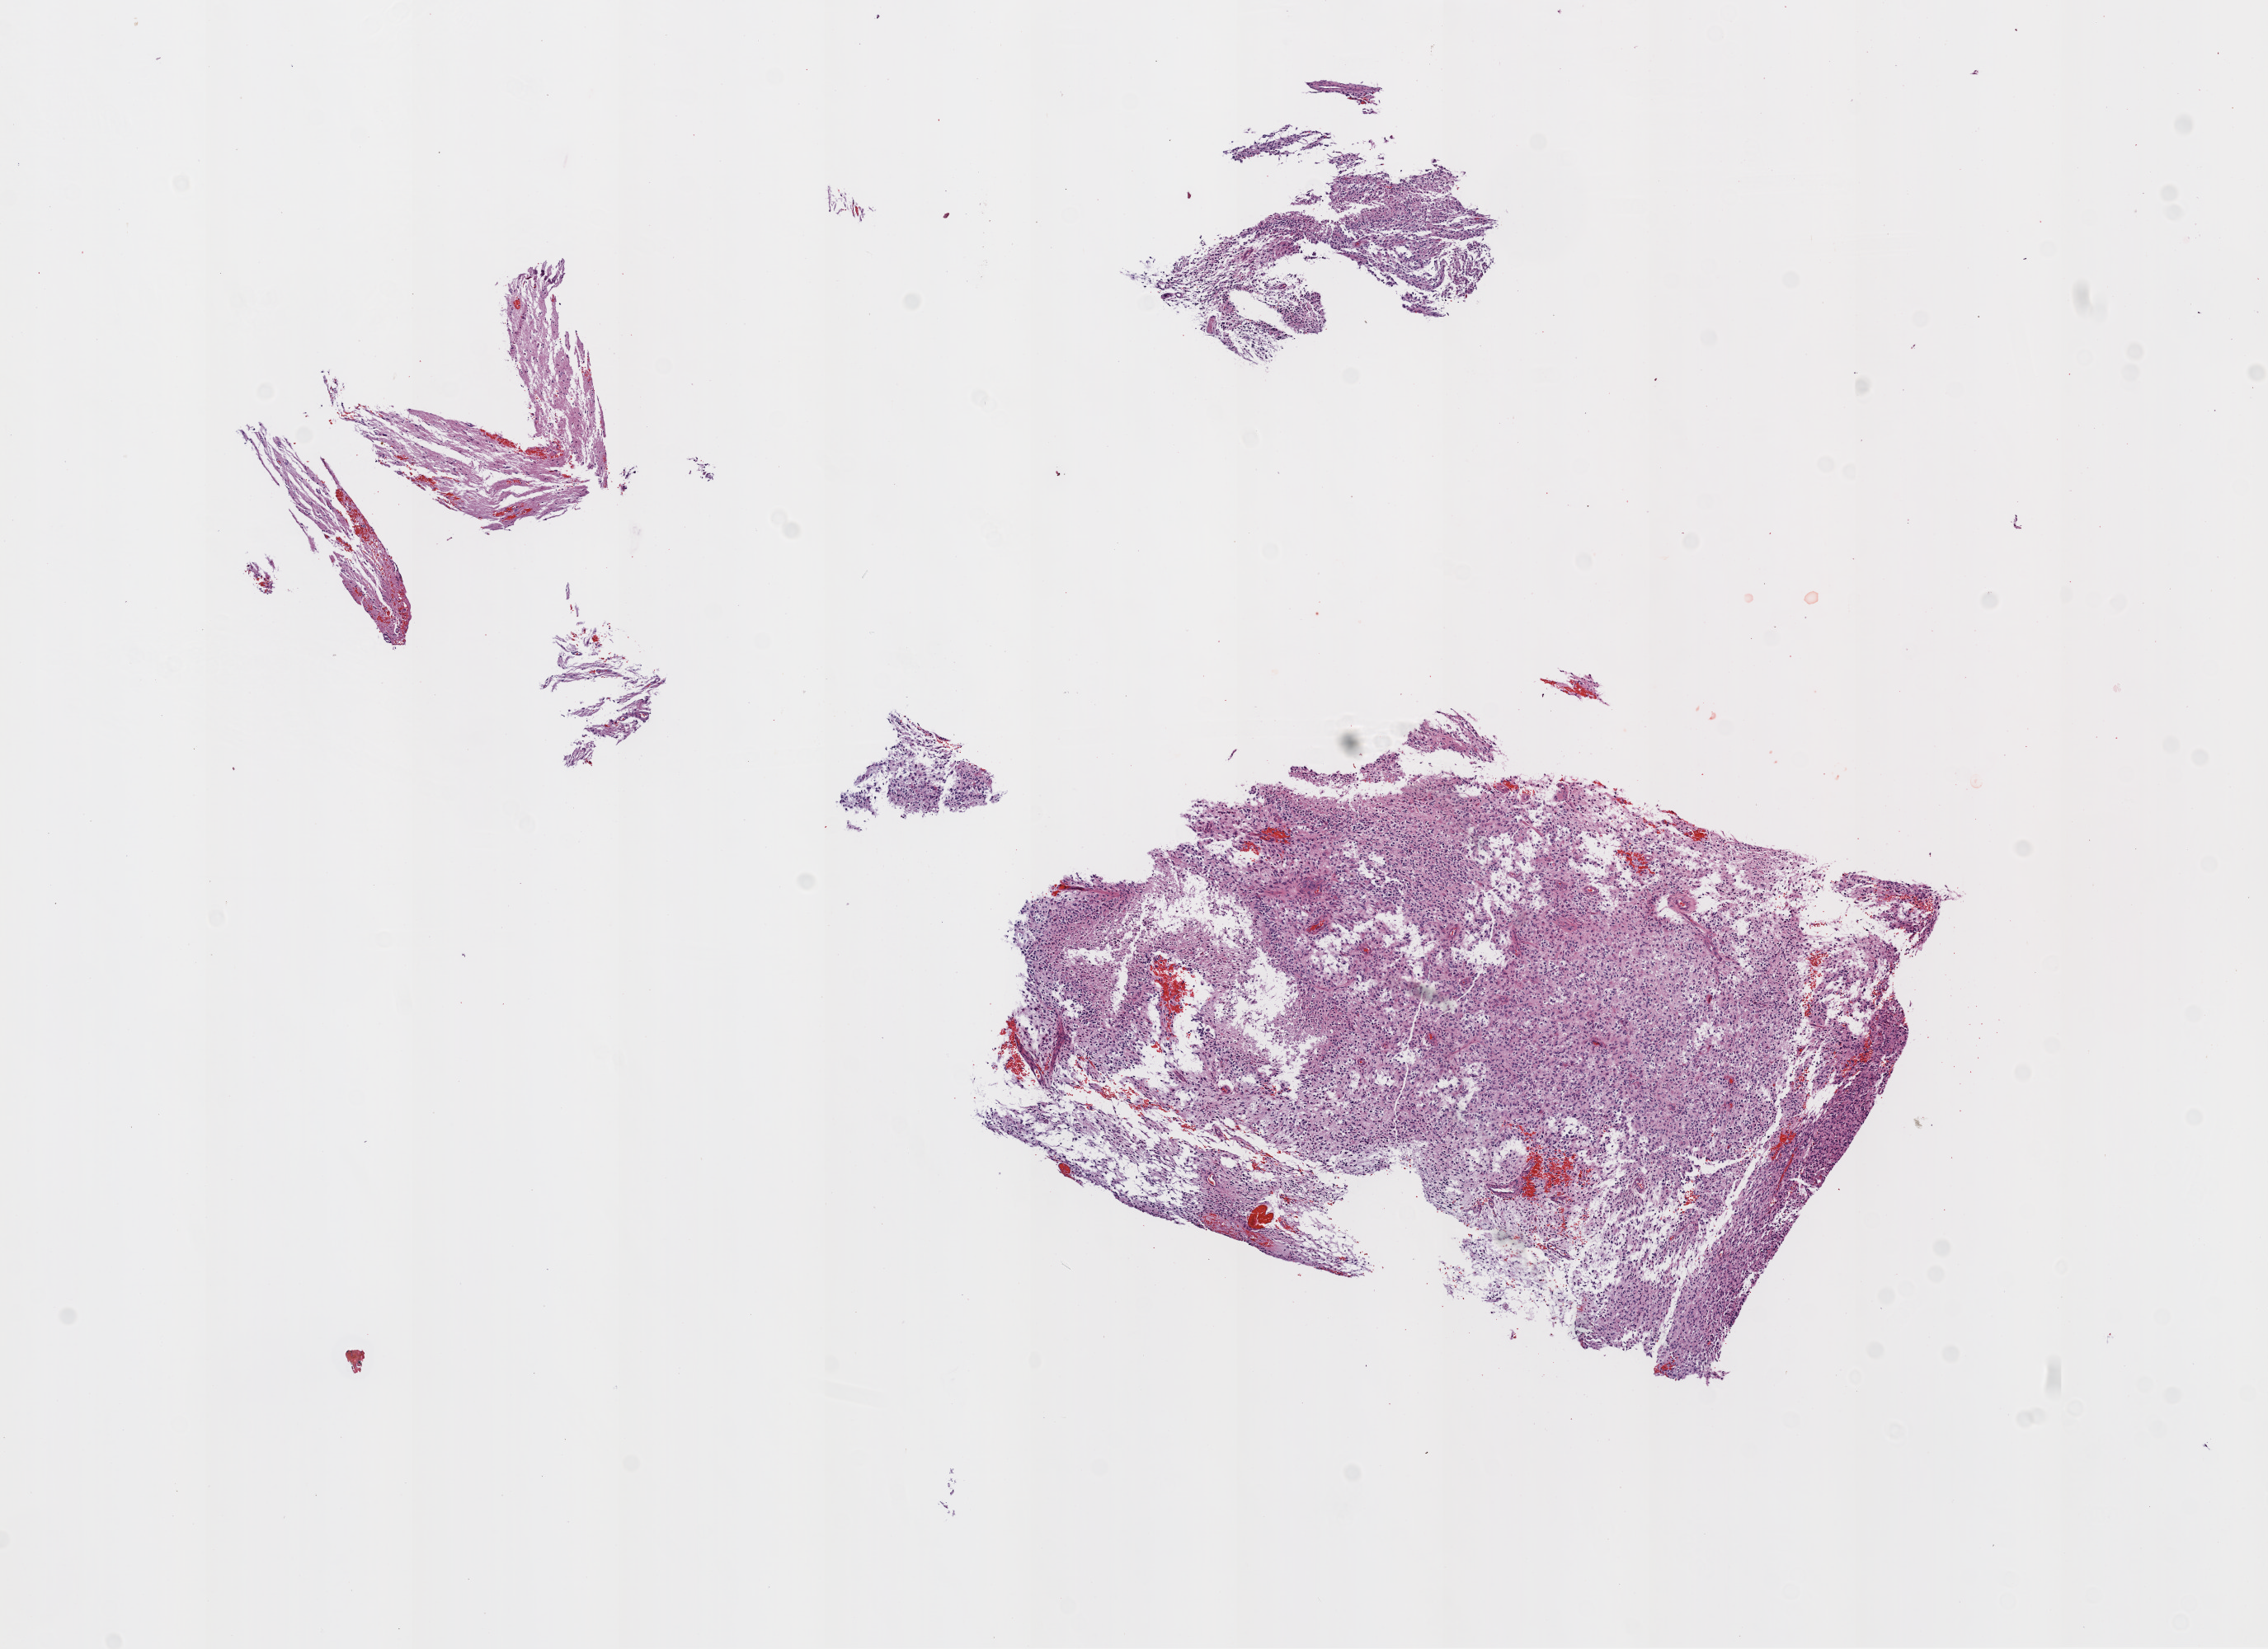
Digitized Hematoxylin and eosin (H&E) stained tissue section (whole slide), shown as a low-resolution overview of the whole scanned area (about 11.0 x 8.0 mm, from a 20x scan), formalin-fixed paraffin-embedded (FFPE) diagnostic section, sample: primary tumour, brain. Patient: female, age at initial diagnosis 55 years.
Histologic diagnosis: Glioblastoma.